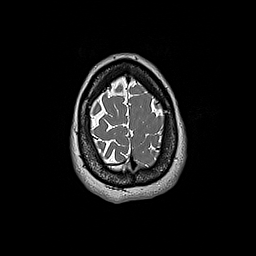
Brain MRI from a brain-tumour surgery series, one axial slice. Slice 45 of 192 in the series (ordered by position). 256 × 256 image matrix, field of view 250 × 250 mm. Case-level facts recorded for this patient, not image findings: histopathology: Glioblastoma; WHO grade: 4.
Annotated regions visible in this slice (expert manual segmentation):
- tumour: bounding box (x1, y1, x2, y2) in pixels: (160, 138, 164, 141)